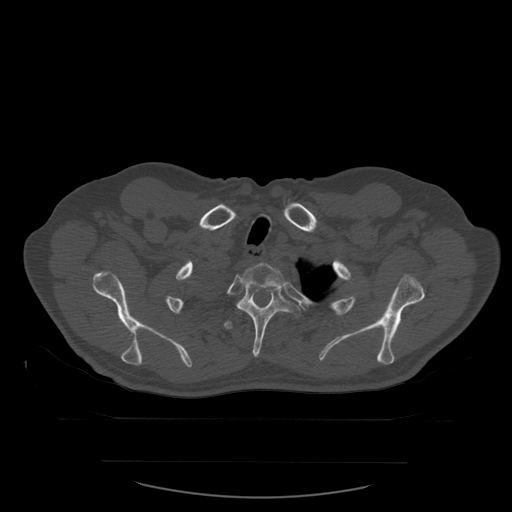
CT including the spine, one axial slice. Slice 461 of 590 in the series (ordered by position). Bone window (W 1800 / L 400 HU). 1.25 mm slice thickness. 512 × 512 image matrix. Patient age 71 years. From the clinical record (not read from this slice): primary cancer: lung; vertebrae with lytic lesions (as recorded): T1, T2, L5, S1.
Structures marked on this image (semi-automatic segmentation, software-assisted and operator-edited):
- T2 vertebra: bounding box (x1, y1, x2, y2) in pixels: (243, 263, 286, 292)
- T3 vertebra: (237, 287, 301, 358)
- T4 vertebra: (223, 320, 234, 330)